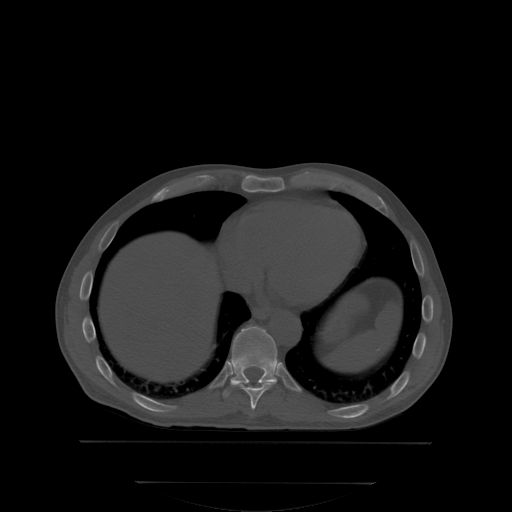
CT including the spine, one axial slice; slice 199 of 350 in the series (ordered by position); bone window (W 1800 / L 400 HU); 512 × 512 image matrix, field of view 500 × 500 mm. Male patient, age 58 years. Case-level facts recorded for this patient, not image findings: primary cancer: prostate; vertebrae with lytic lesions (as recorded): L1.
Annotated regions visible in this slice (semi-automatic segmentation, software-assisted and operator-edited):
- T10 vertebra: bounding box (x1, y1, x2, y2) in pixels: (225, 326, 278, 396)
- T9 vertebra: (232, 383, 274, 410)